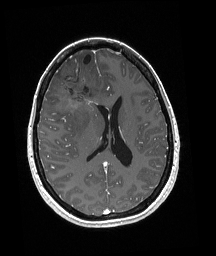
Brain MRI from a brain-tumour surgery series, one axial slice; position 84 of 192 along the scan axis; T1-weighted post-contrast; 1 mm slice thickness; 216 × 256 image matrix, field of view 211 × 250 mm. From the clinical record (not read from this slice): histopathology: Oligodendroglioma; WHO grade: 3; IDH mutation: yes; tumour location: Right Frontal.
Structures marked on this image (outlined manually by an expert reader):
- tumour: box from (x=55, y=80) to (x=99, y=114) px